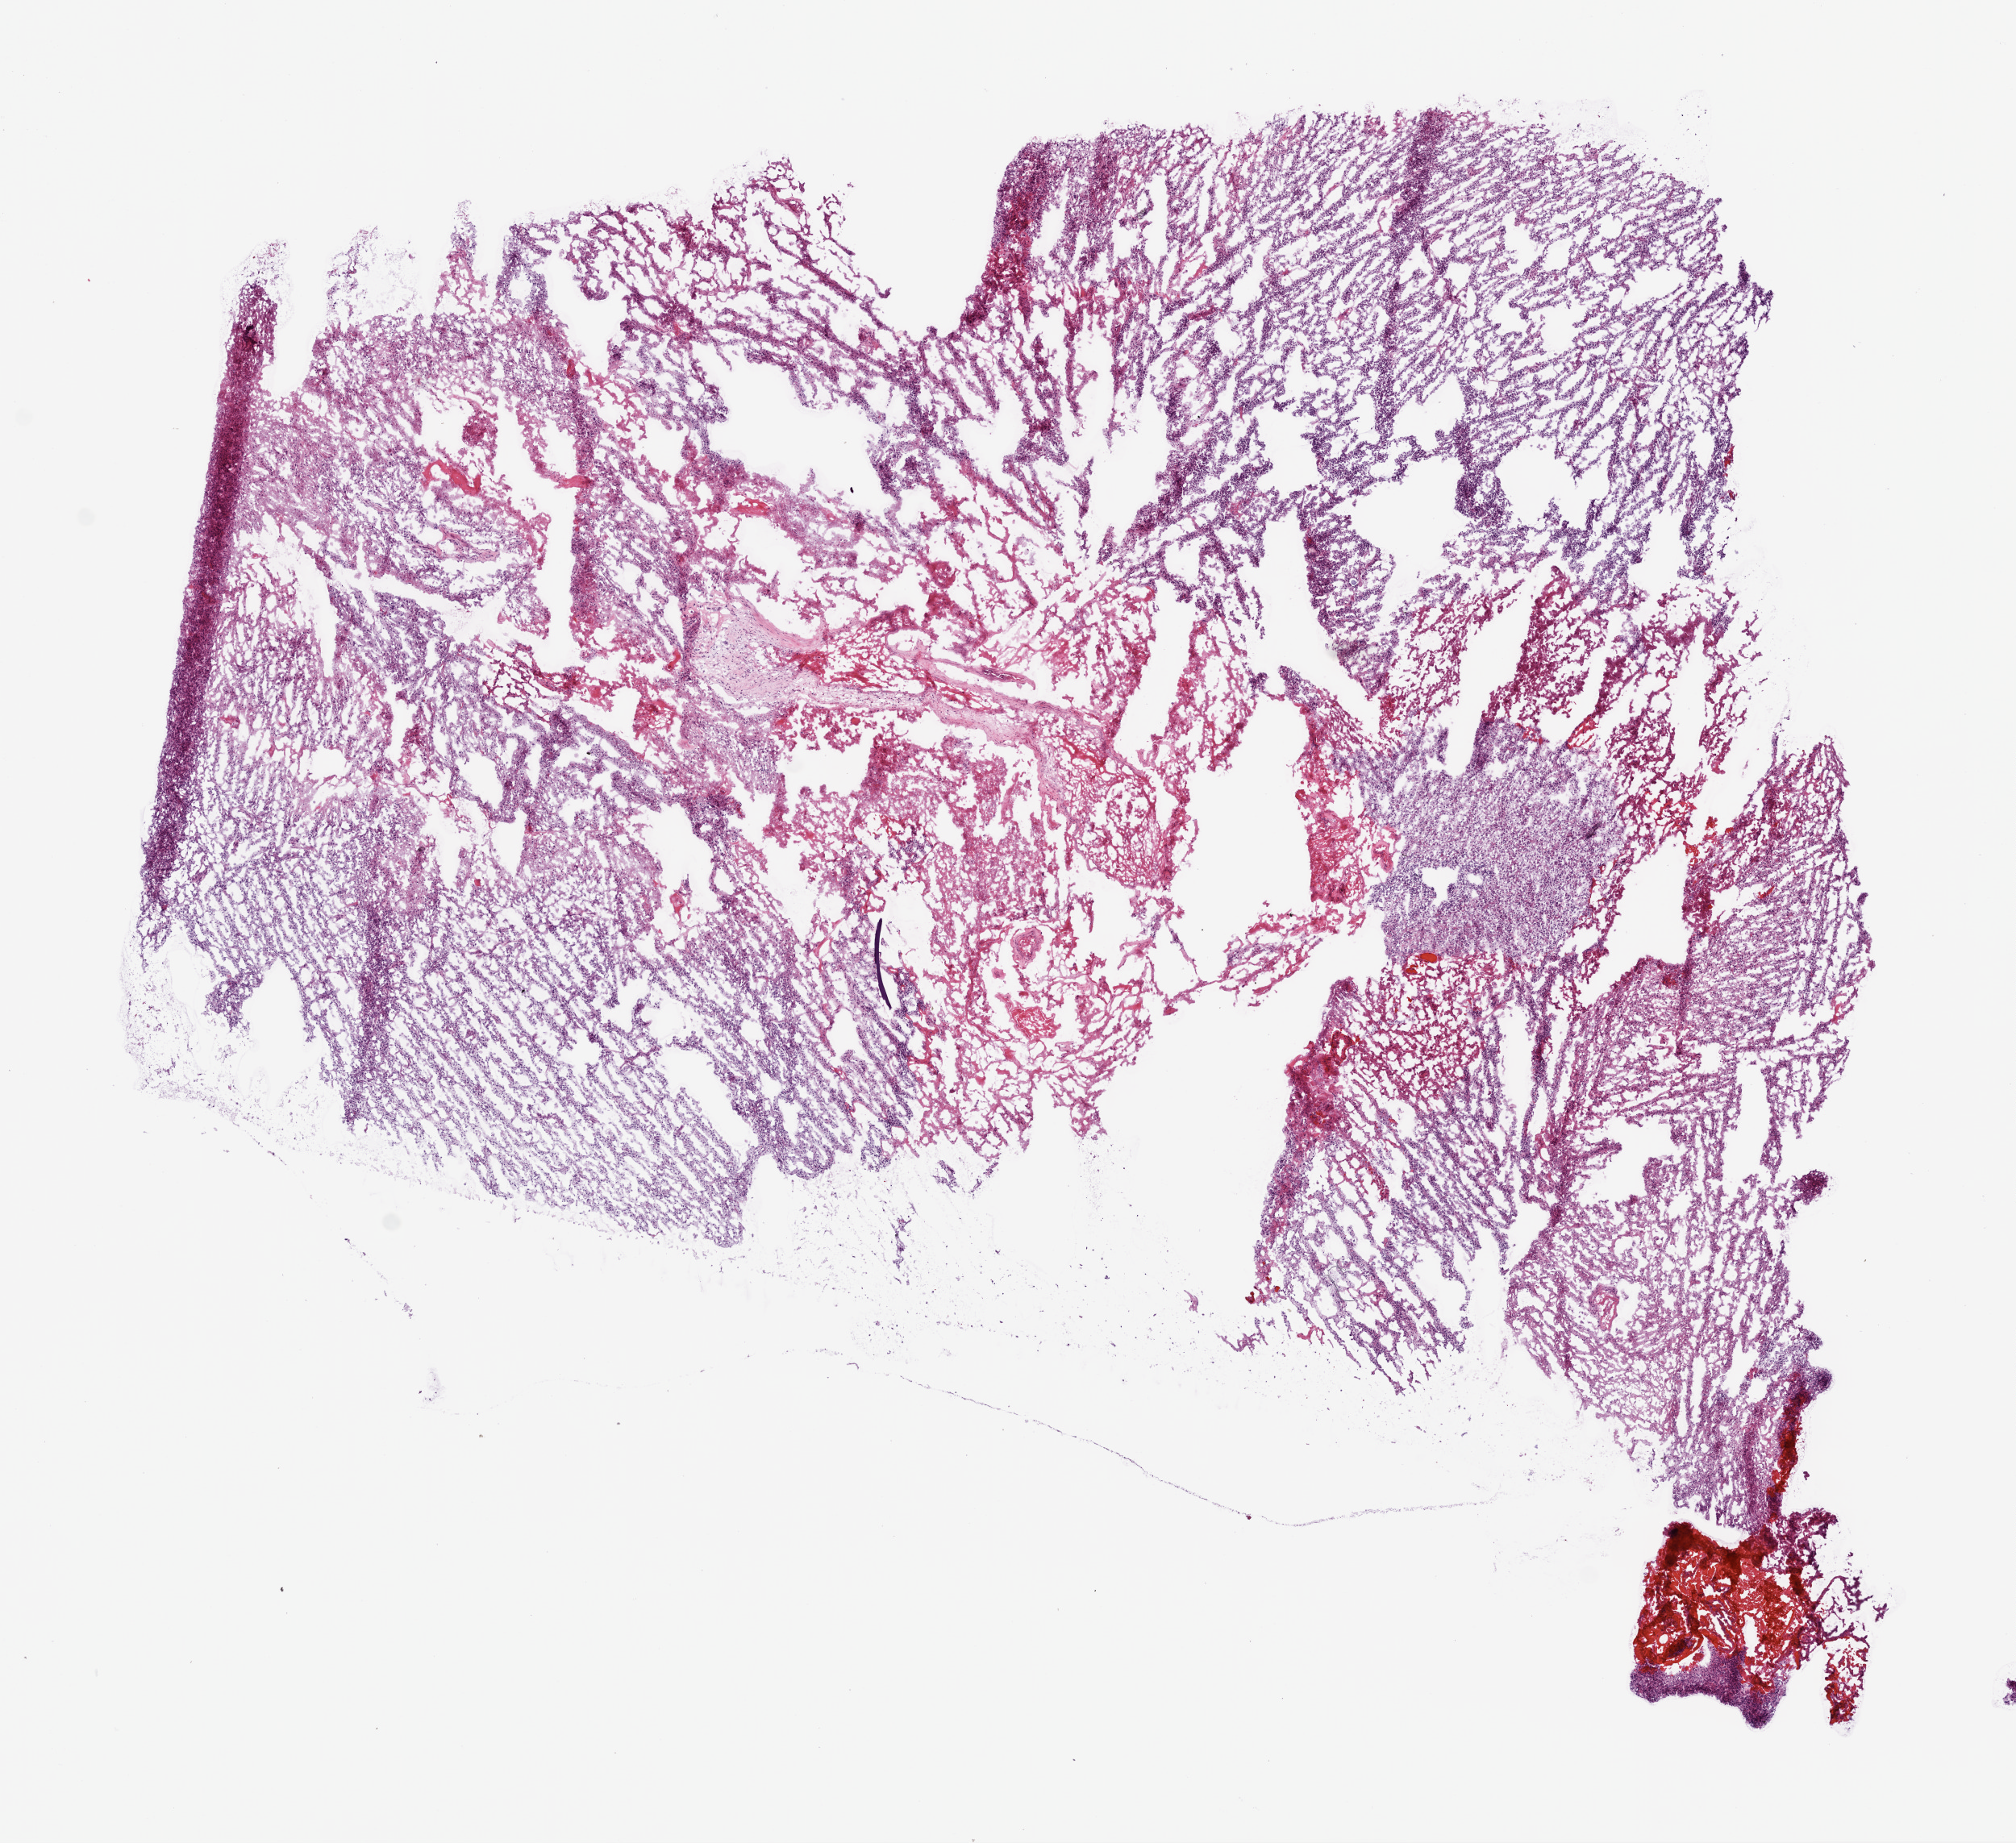
Whole-slide histology image, Hematoxylin and eosin (H&E) stained — whole scanned area (about 10.0 x 9.2 mm, from a 20x scan) shown as a low-resolution overview. Frozen section from the bottom of the tissue portion. Sample: primary tumour, brain. Patient: male, age at initial diagnosis 74 years. Slide review estimates, as recorded: tumour cells 75%, tumour nuclei 80%, normal cells 0%, stromal cells 0%, necrosis 25%.
* histologic diagnosis: Glioblastoma